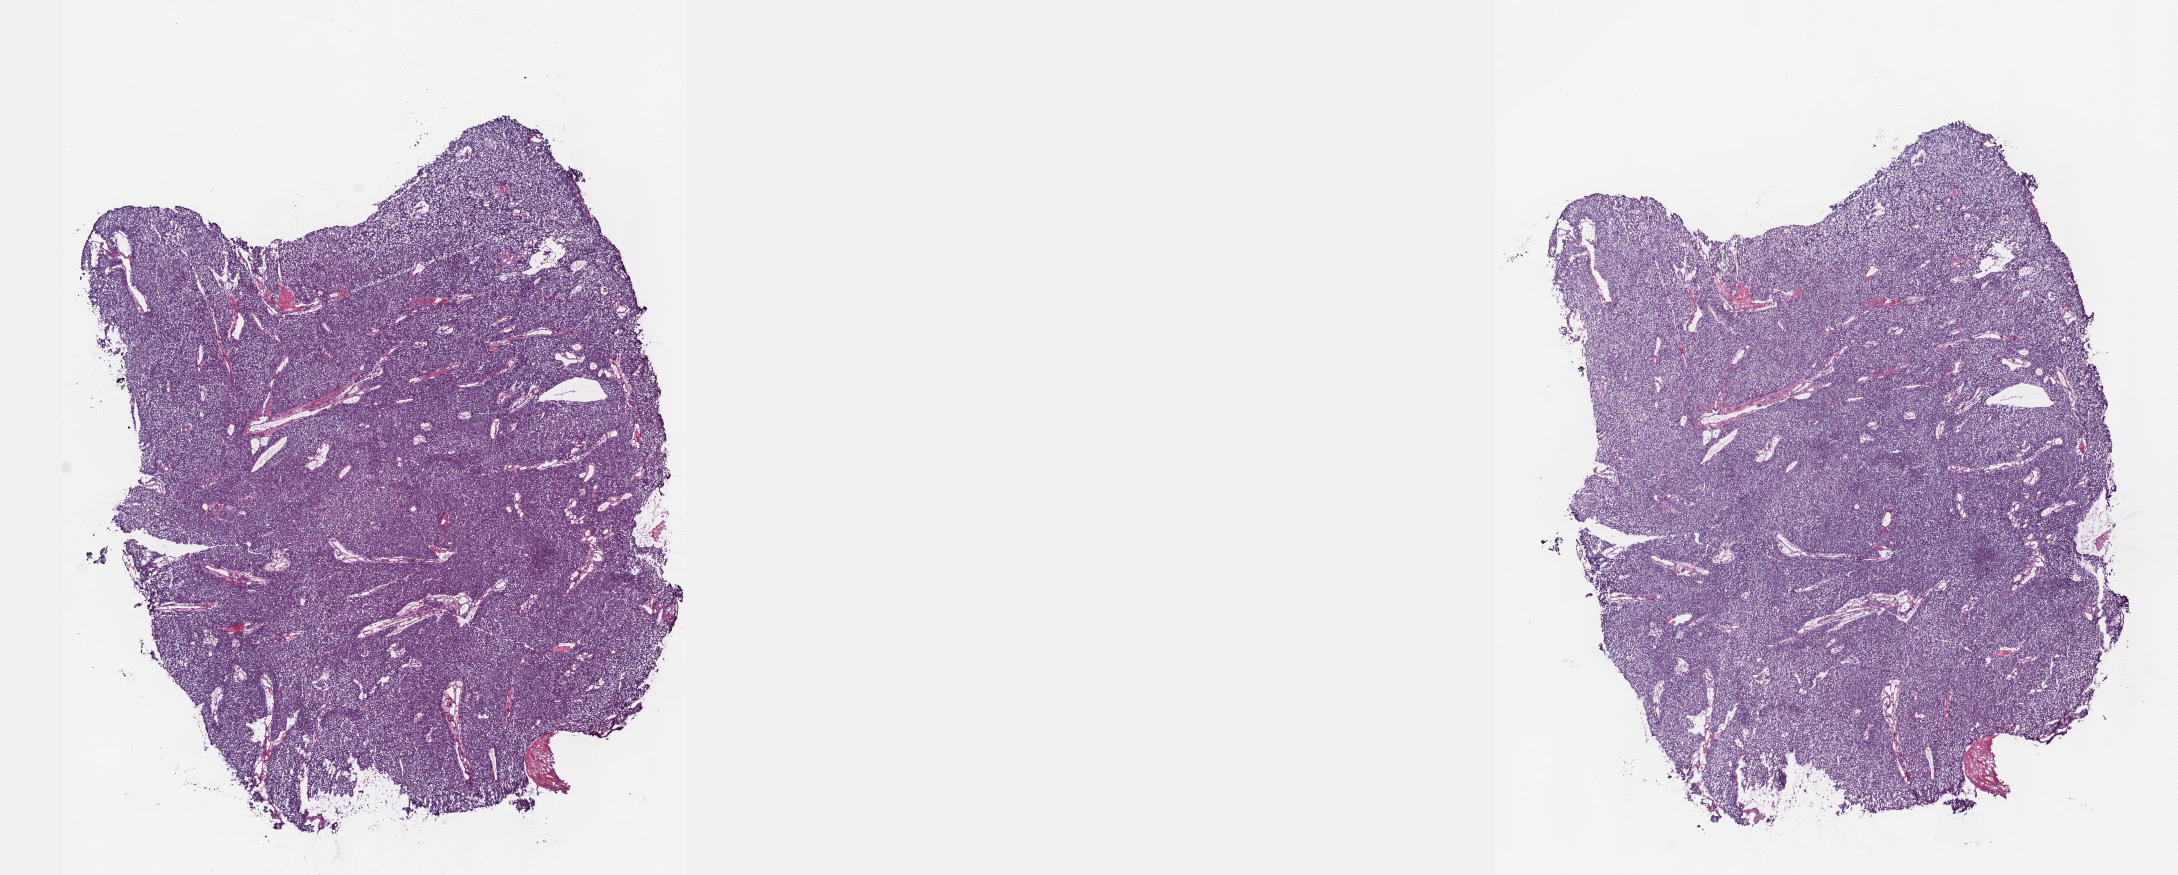
H&E-stained whole-slide image, low-resolution overview of the scanned area, about 17.6 x 7.1 mm (slide scanned at 40x). Frozen section. Thymus, primary tumour sample. Female, age 64 years at initial diagnosis. Slide review estimates, as recorded: tumour cells 100%, tumour nuclei 80%, normal cells 0%, stromal cells 0%, necrosis 0%. Infiltration values recorded for this section: lymphocyte infiltration 4%, monocyte infiltration 0%, neutrophil infiltration 0%.
Histologic diagnosis: Thymoma, type B3, malignant.